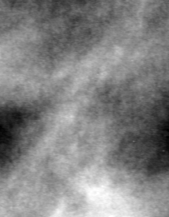
Crop from a digitized film mammogram around one marked abnormality, left breast, MLO view.
Calcifications, morphology fine linear branching, distribution linear; BI-RADS assessment category 4; subtlety rating 1 on a 1 (subtle) to 5 (obvious) scale; pathology result (as recorded, not read from the image): malignant.